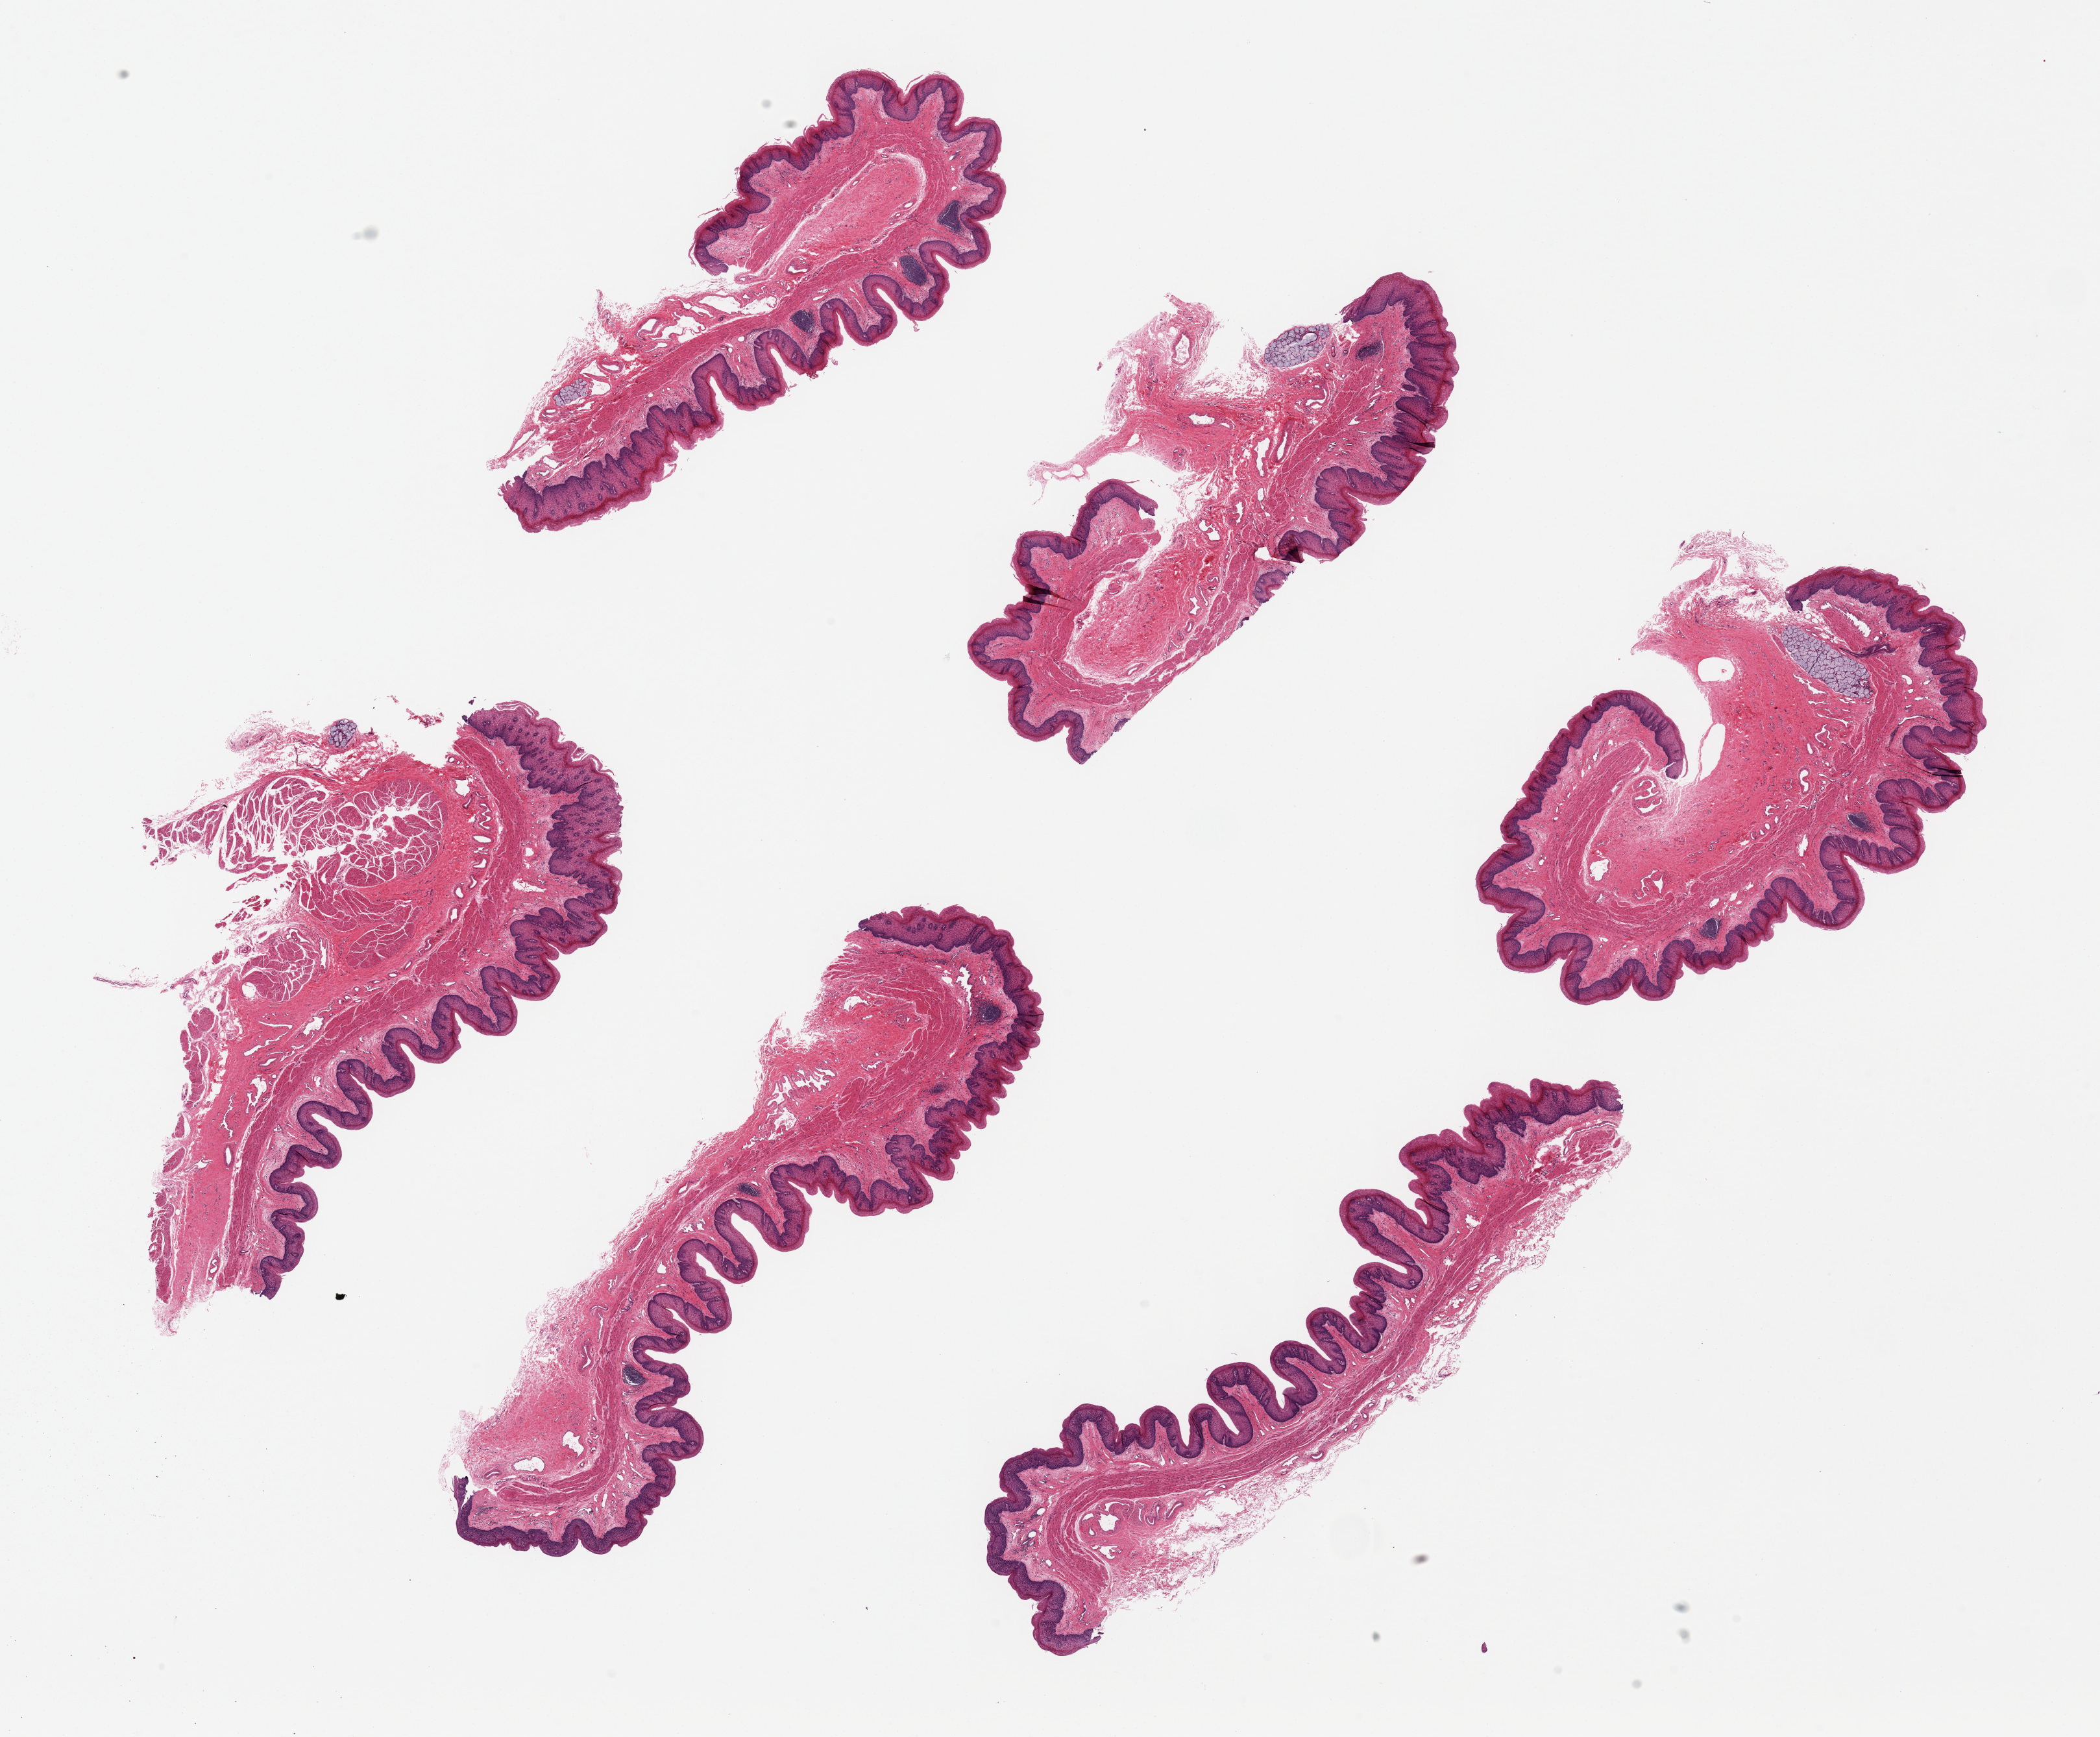
Haematoxylin and eosin whole-slide image, brightfield, shown as a low-resolution overview of the whole scanned area (about 25.6 x 21.2 mm, from a 20x scan), PAXgene-fixed, paraffin-embedded tissue, target tissue: esophageal mucous membrane, tissue donor sample. Donor sex: male.
Pathologist's review note for this sample: 6 pieces ~8x2.5mm; Squamous mucosa is ~10-20% of thickness; occasional sub-mucosal glands noted; Focal chronic inflammation.